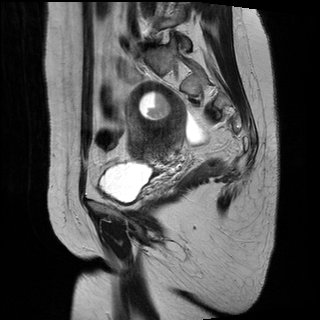
Pelvic MRI for cervical cancer, one sagittal slice; slice 21 of 34 in the series (ordered by position); T2-weighted; 1.5 T; TE 89 ms, TR 3320 ms; 320 × 320 image matrix, field of view 260 × 260 mm. Female patient, age 49 years.
Outlined on this slice (outlined manually by an expert reader):
- uterus and cervix: bounding box (x1, y1, x2, y2) in pixels: (124, 81, 189, 163)